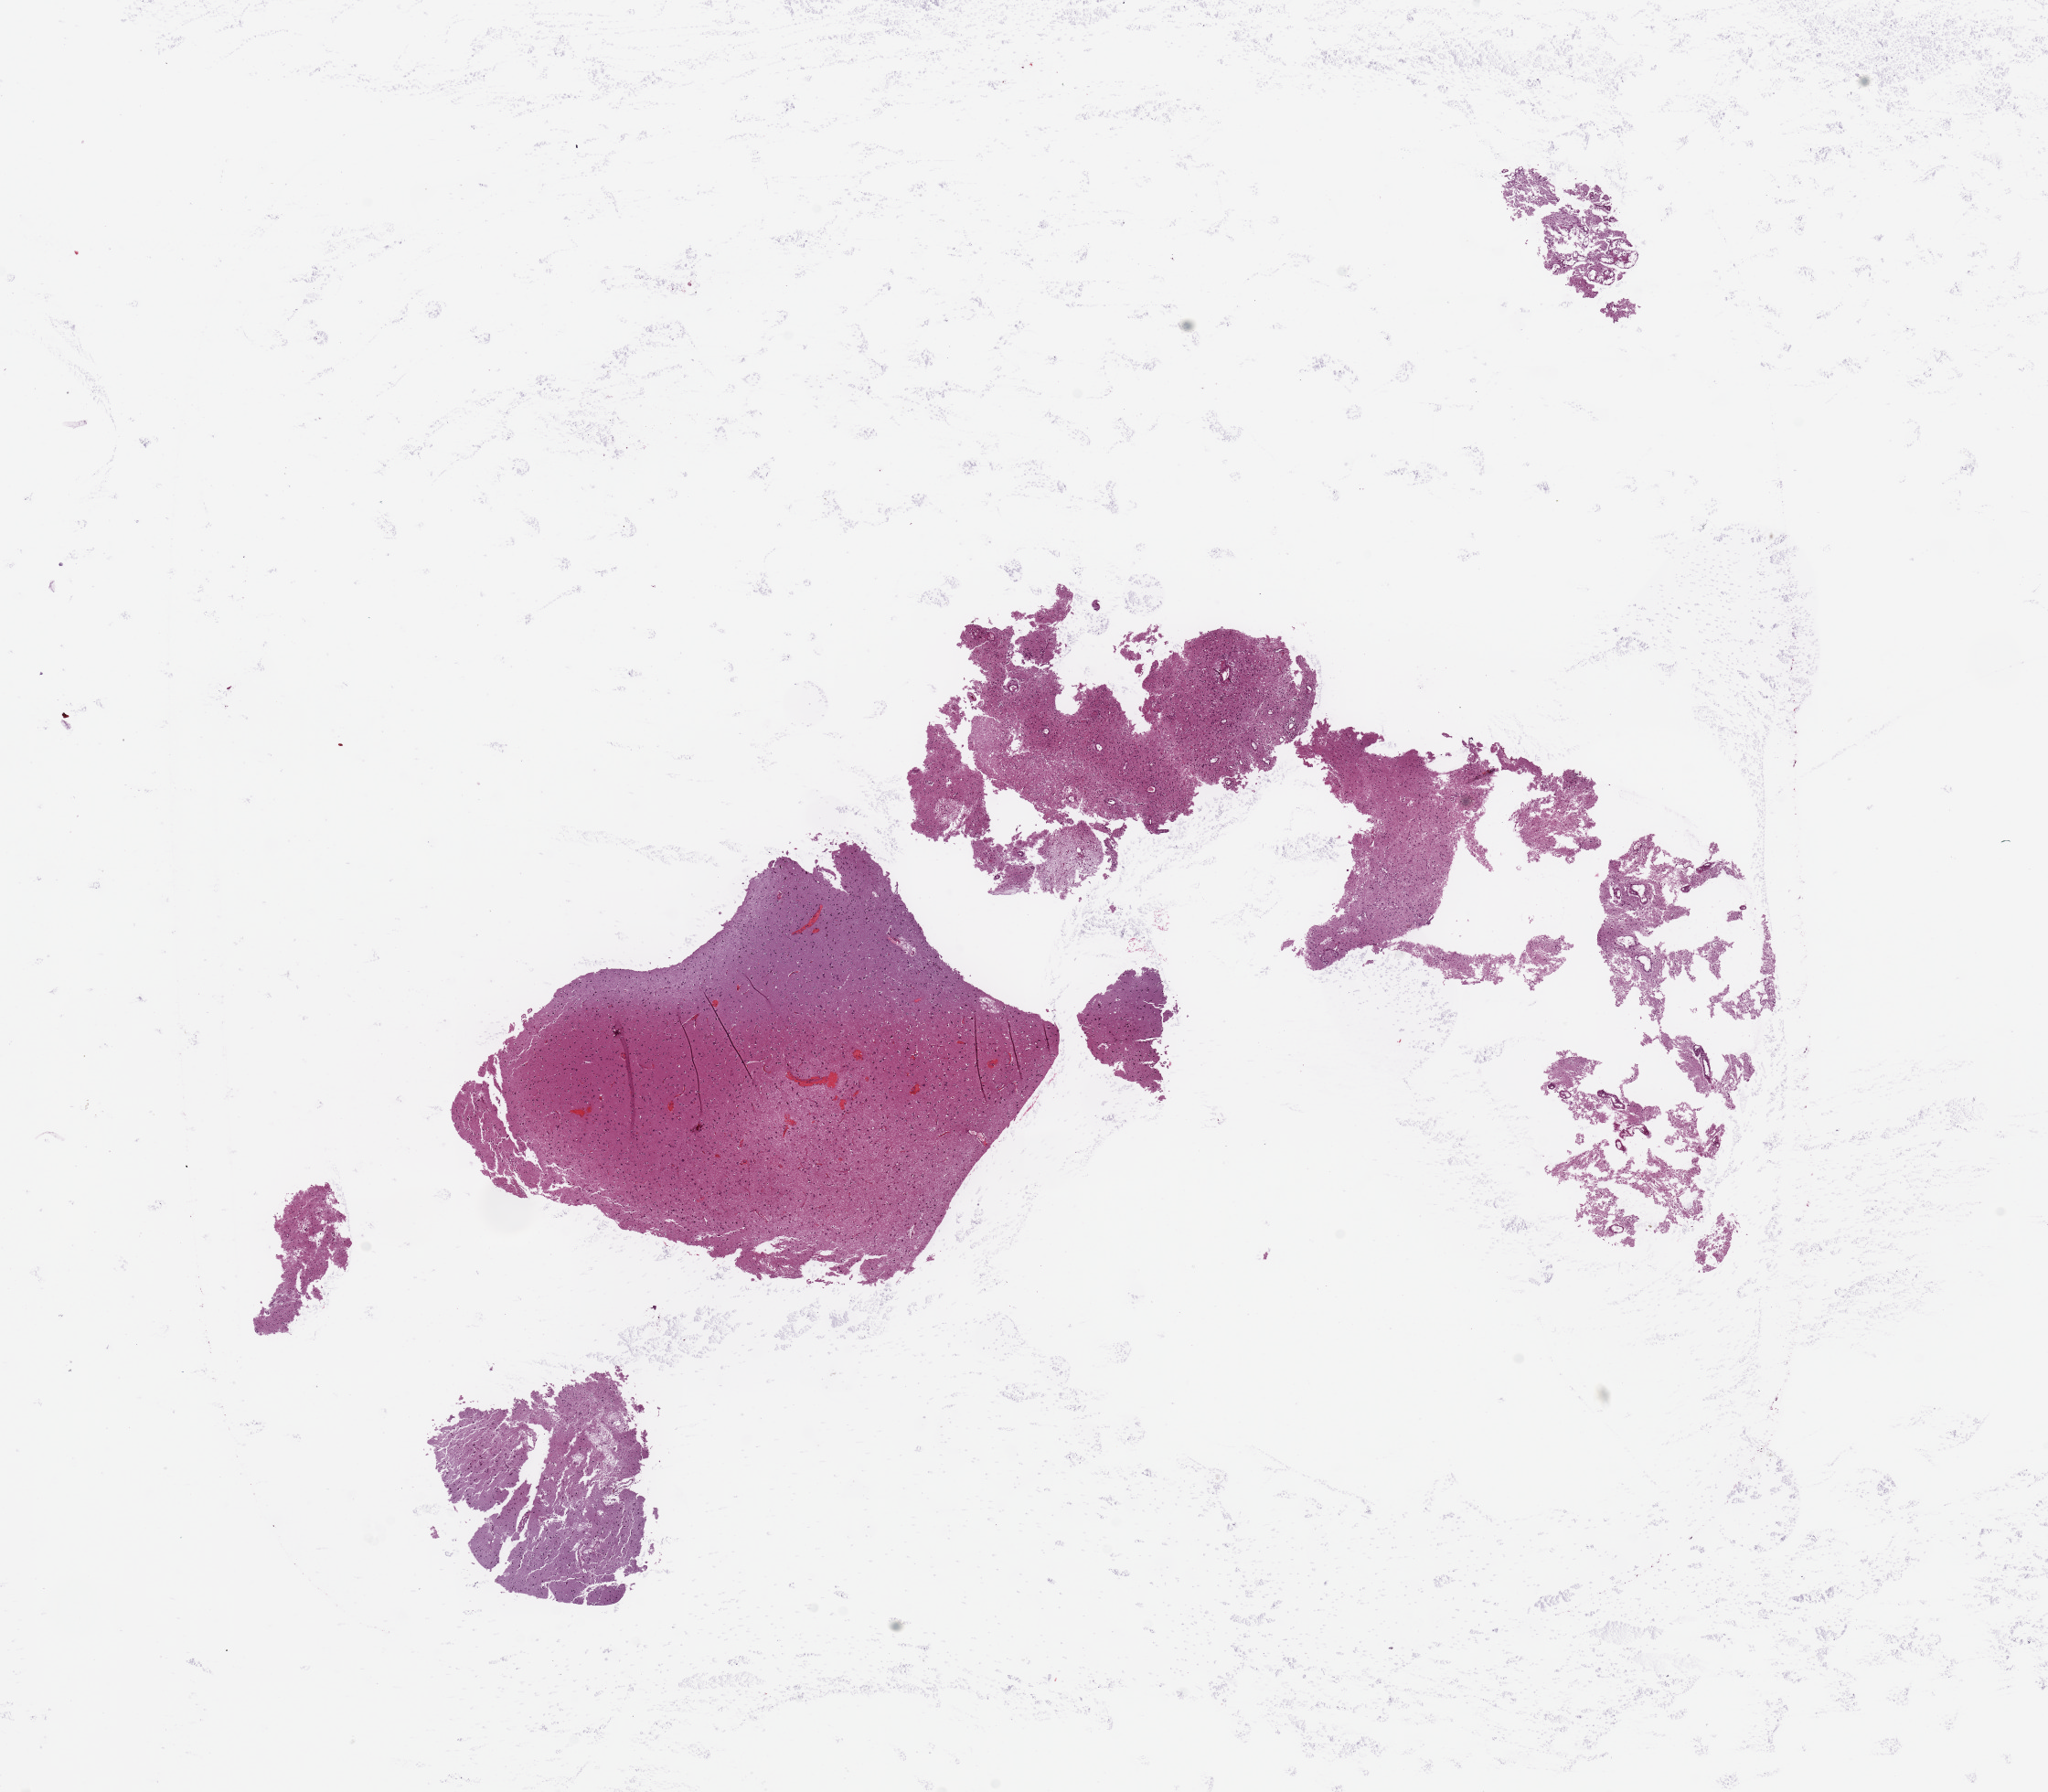
Whole-slide histology image, H&E — a low-resolution overview of the entire scanned area, about 17.7 x 15.5 mm (acquisition: 20x scan), brain, tumour tissue. Patient: male, age 53 years.
Histologic diagnosis: Glioblastoma.